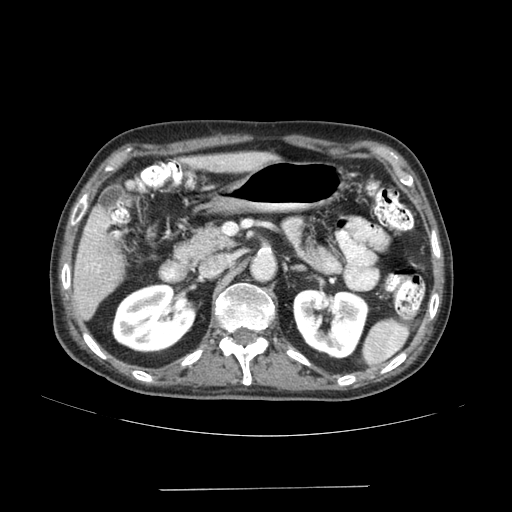
Contrast-enhanced abdominal CT (liver protocol), one axial slice. Slice 72 of 192 in the series (ordered by position). Reconstruction kernel SOFT. Soft-tissue window (W 400 / L 40 HU). 512 × 512 image matrix, field of view 400 × 400 mm. From the clinical record (not read from this slice): diagnosis: hepatocellular carcinoma (patient treated with transarterial chemoembolisation; whether this scan precedes or follows treatment is not stated here); TNM stage (as recorded): Stage-IVA; Child-Pugh class: A; tumour differentiation: poorly differentiated; tumour nodularity: uninodular.
Annotated regions visible in this slice (semi-automatically segmented with operator editing):
- liver parenchyma outside the tumour (the mass and vessels are separate outlines, so this box may not span the whole liver): bounding box (x1, y1, x2, y2) in pixels: (74, 152, 275, 320)